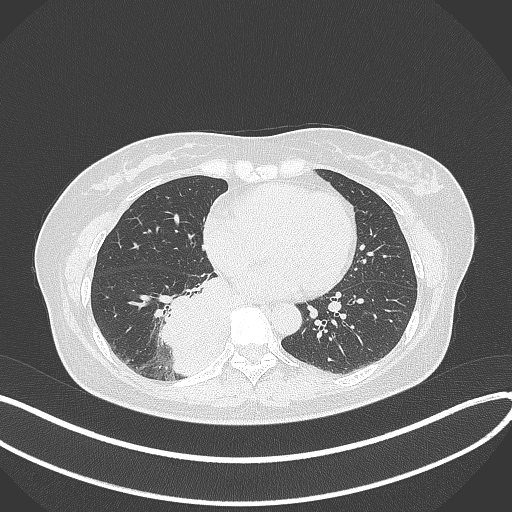
Chest CT, one axial slice. Slice 139 of 331 in the series (ordered by position). Lung window (W 1500 / L -600 HU). 1 mm slice thickness. 512 × 512 image matrix, field of view 400 × 400 mm. Female patient, age 54 years. From the clinical record (not read from this slice): clinical TNM (as recorded): T4 N0 M0.
Annotated regions visible in this slice (bounding box drawn by a radiologist):
- lung tumour (recorded histology: adenocarcinoma): box from (x=156, y=271) to (x=237, y=378) px